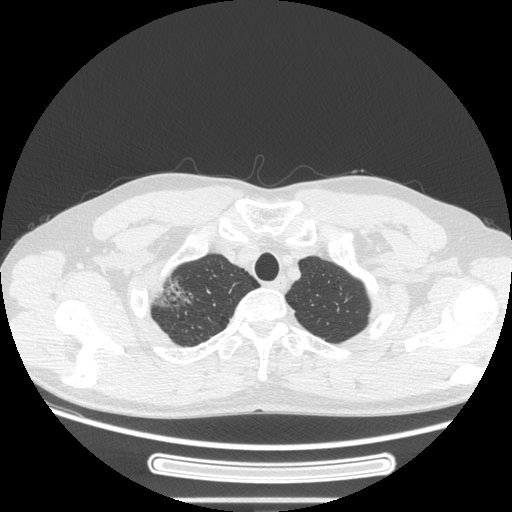
Chest CT, one axial slice; position 234 of 269 along the scan axis; reconstruction kernel STANDARD; 120 kVp; lung window (W 1500 / L -600 HU); 1.25 mm slice thickness; 512 × 512 image matrix, field of view 382 × 382 mm. Male patient, age 53 years. Case-level facts recorded for this patient, not image findings: clinical TNM (as recorded): T1c N0 M0; histopathological grade: G2.
Structures marked on this image (bounding box drawn by a radiologist):
- lung tumour (recorded histology: adenocarcinoma): bounding box <144,263,201,321> (left, top, right, bottom; pixels)